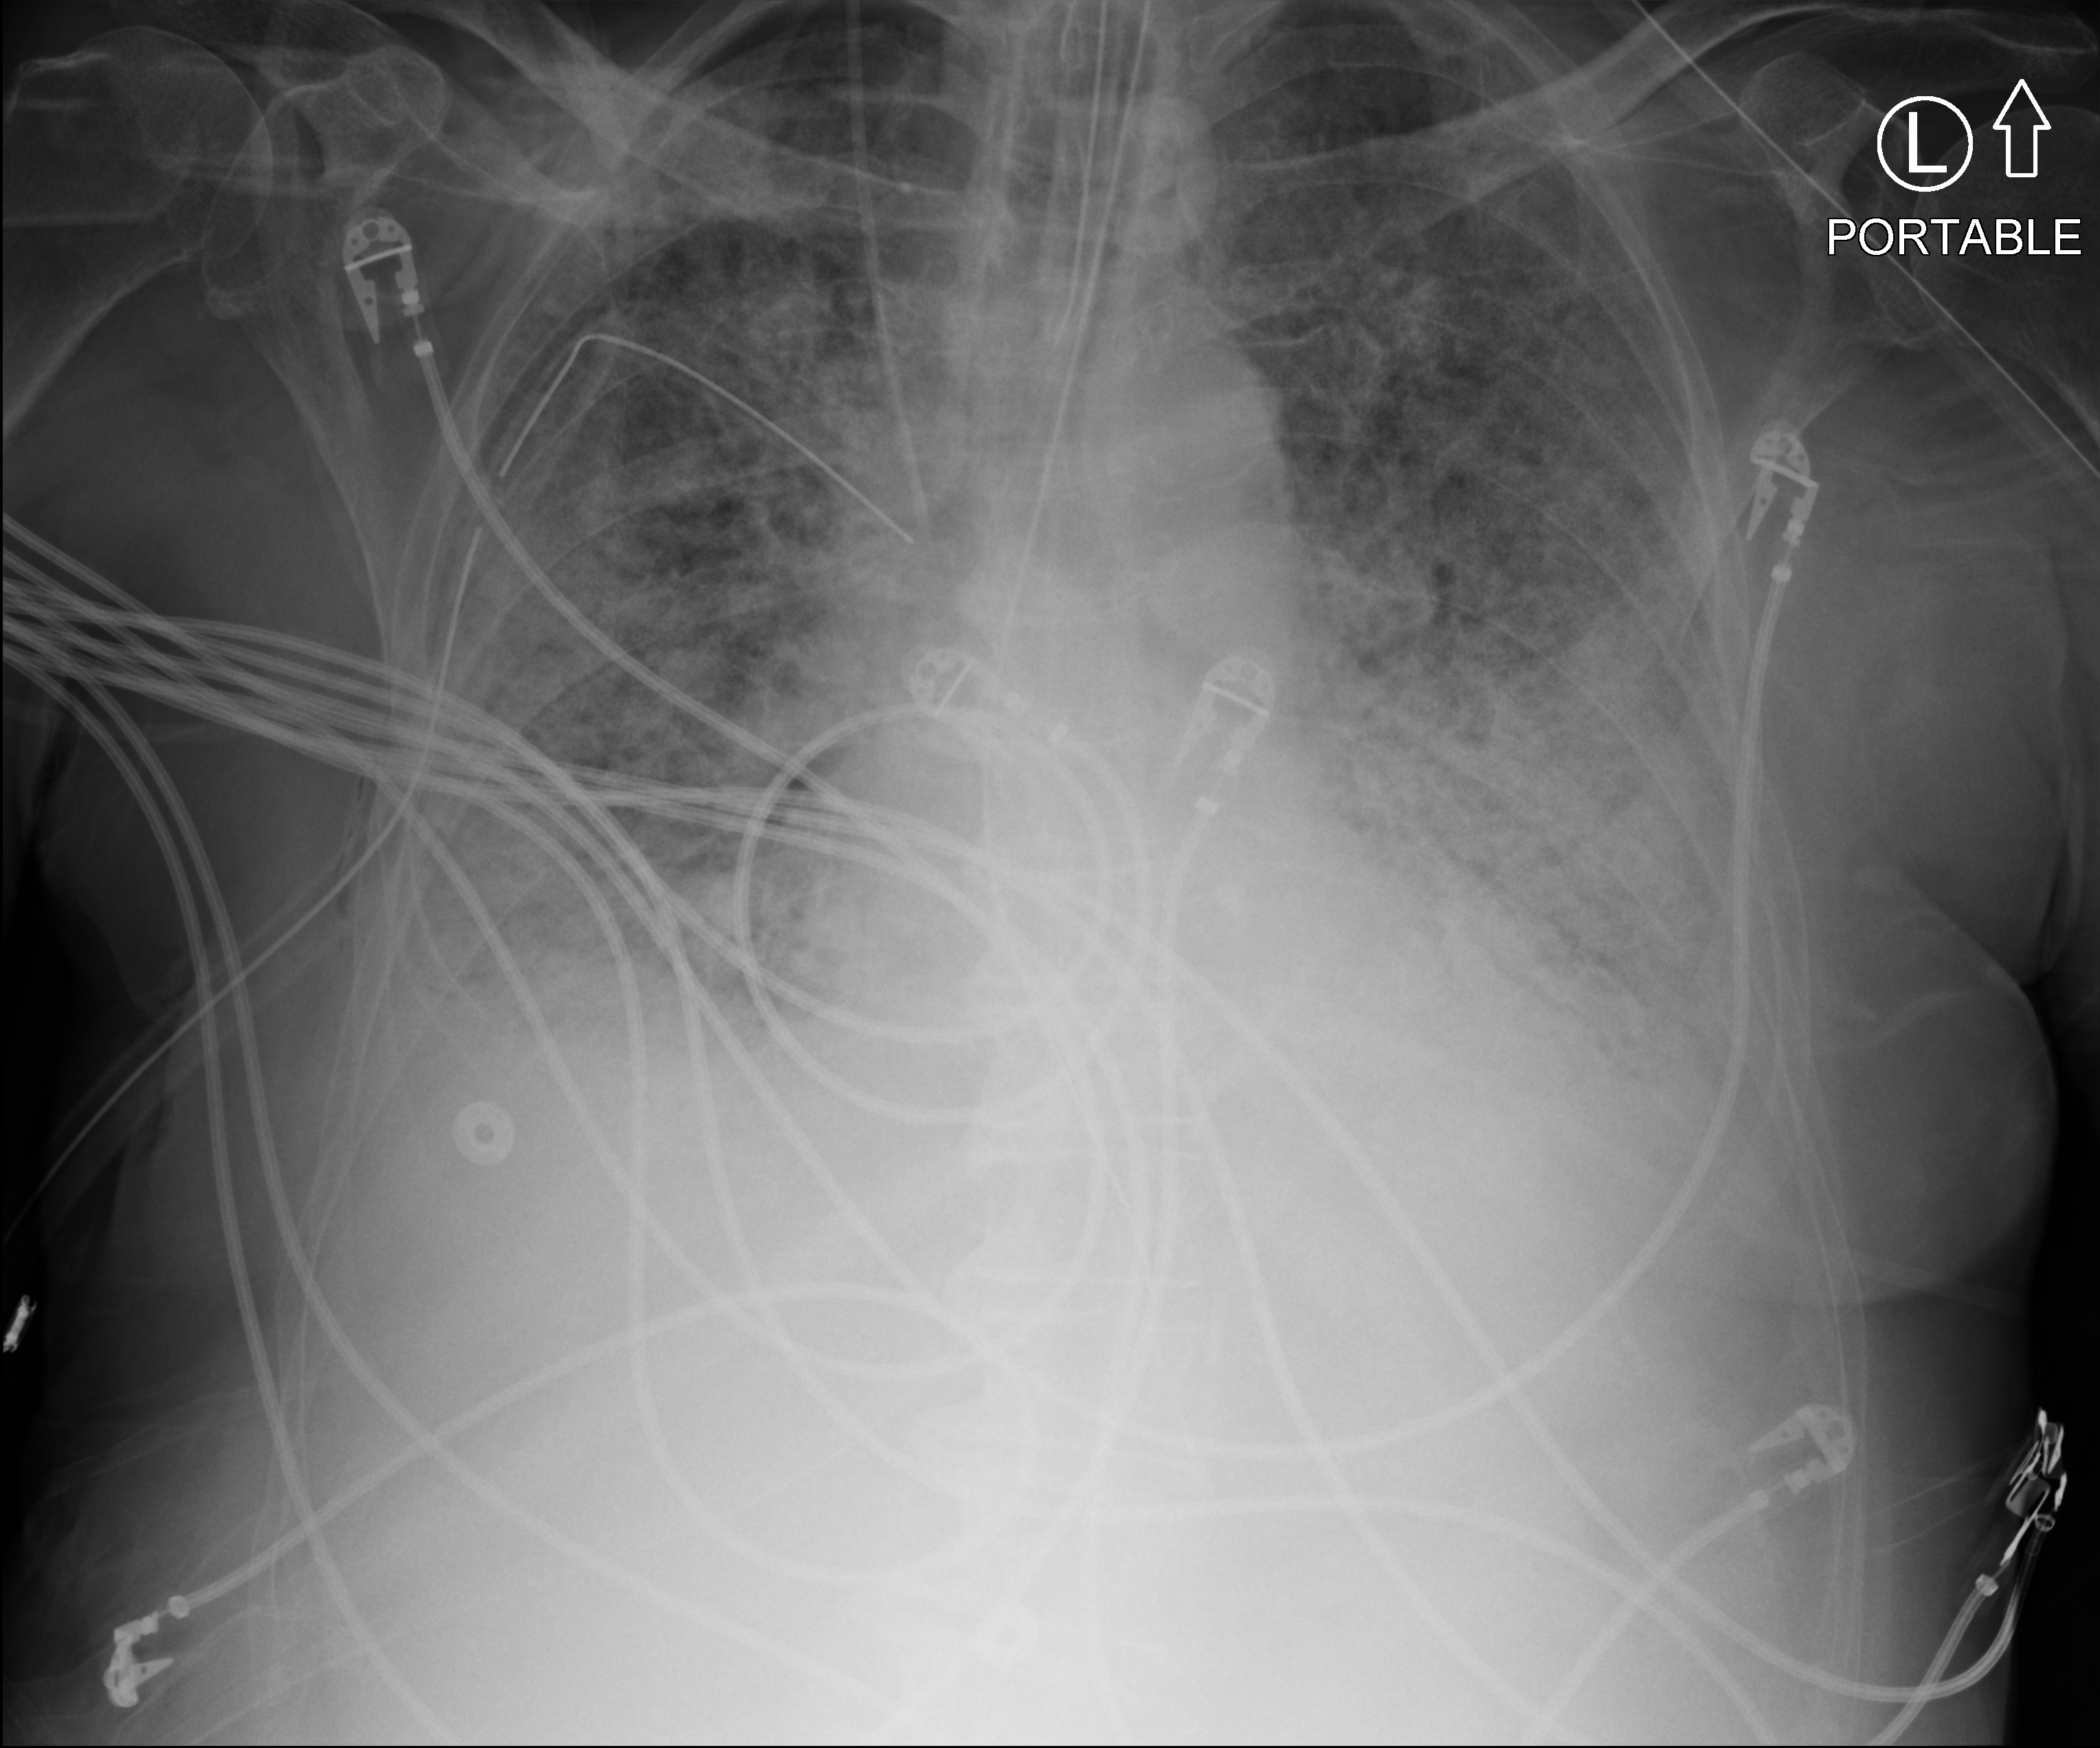
Bedside chest radiograph (computed radiography), anteroposterior (AP) projection. Patient hospitalised with COVID-19; male, aged 75–90 years.
Hospital-stay facts (about this admission, not read from this image; timing relative to this image not recorded): mechanically ventilated during this hospital stay: yes.